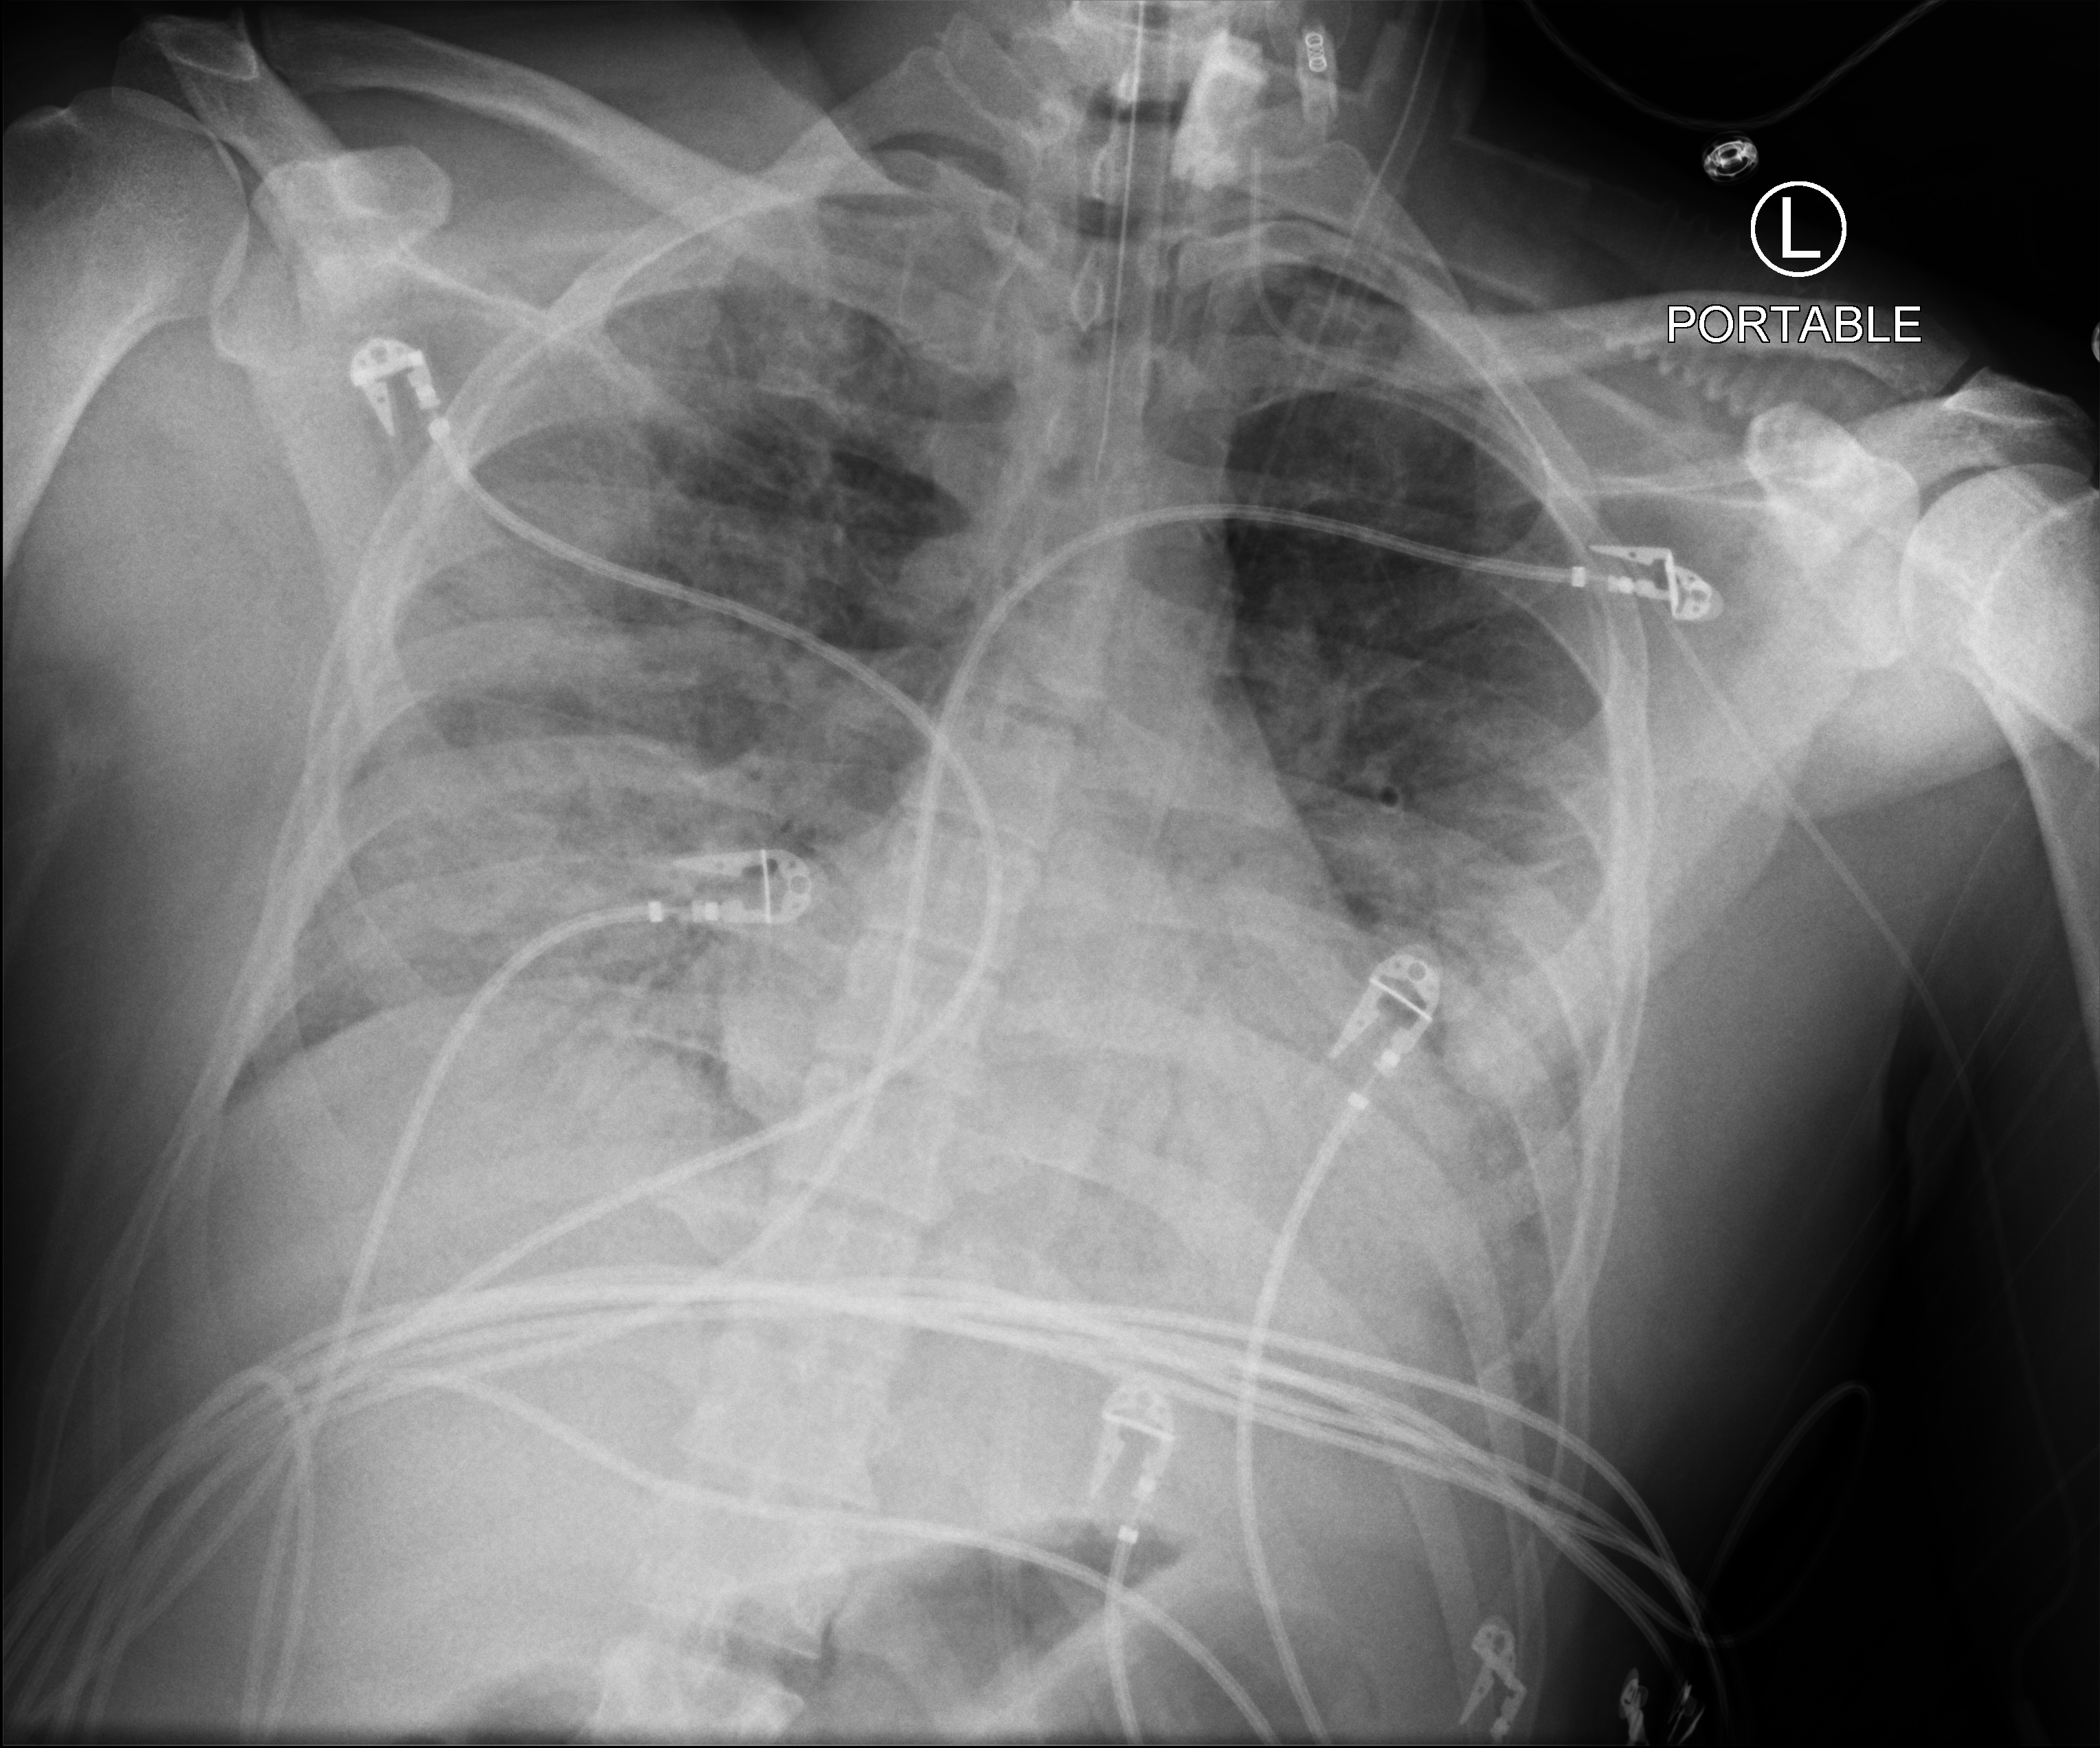
Portable chest radiograph; anteroposterior (AP) projection. Patient hospitalised with COVID-19; male, aged 18–59 years.
Hospital-stay facts (about this admission, not read from this image; timing relative to this image not recorded):
- admitted to intensive care during this hospital stay: yes
- length of hospital stay: 30 days
- COPD (admission record): no